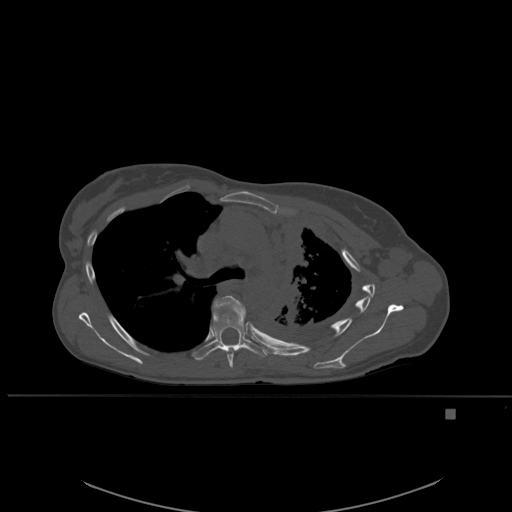
CT including the spine, one axial slice. Slice 389 of 537 in the series (ordered by position). Bone window (W 1800 / L 400 HU). 1.5 mm slice thickness. 512 × 512 image matrix, field of view 440 × 440 mm. Female patient, age 45 years. Case-level facts recorded for this patient, not image findings: primary cancer: lung.
Annotated regions visible in this slice (semi-automatic segmentation, software-assisted and operator-edited):
- T5 vertebra: box from (x=213, y=295) to (x=246, y=368) px
- T6 vertebra: (x=196, y=312)–(x=269, y=361)